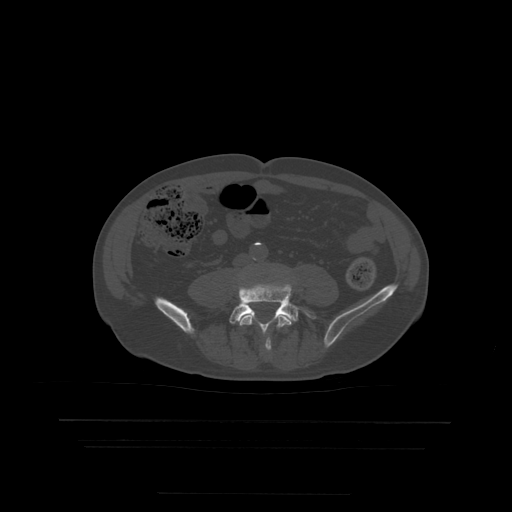
CT including the spine, one axial slice. Position 82 of 522 along the scan axis. Bone window (W 1800 / L 400 HU). 512 × 512 image matrix, field of view 436 × 436 mm. Patient age 68 years. Case-level facts recorded for this patient, not image findings: primary cancer: urothelial.
Structures marked on this image (semi-automatically segmented with operator editing):
- L4 vertebra: bounding box (x1, y1, x2, y2) in pixels: (240, 312, 292, 351)
- L5 vertebra: (221, 285, 317, 341)